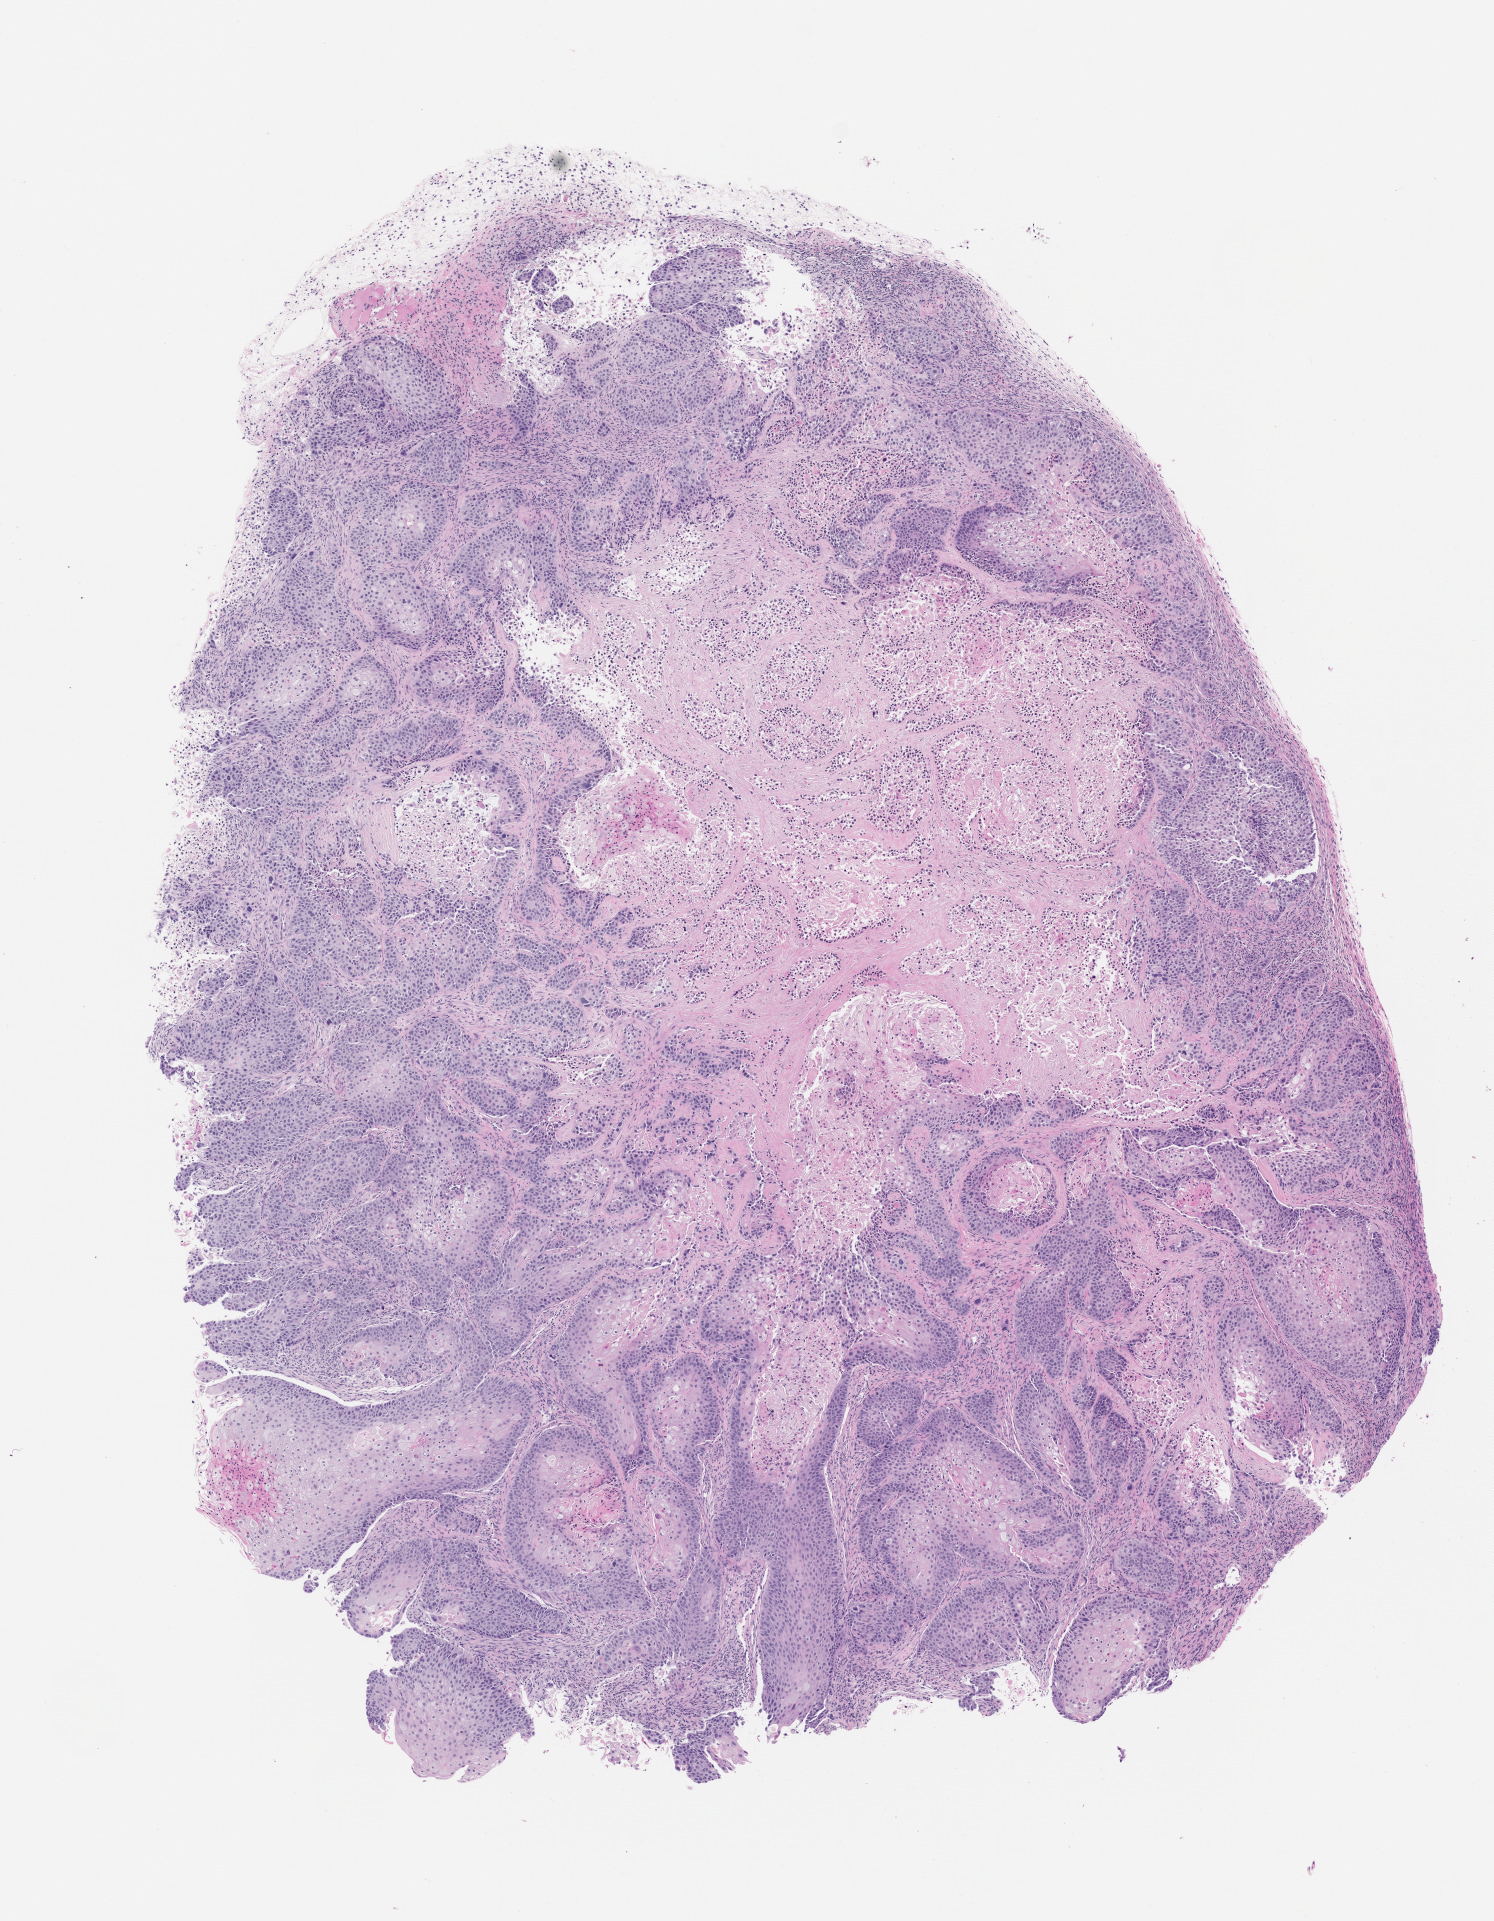
H&E whole-slide image of a patient-derived xenograft (PDX) tumor grown in a mouse, passage 2, a low-resolution overview of the entire scanned area, about 6.0 x 7.7 mm. FFPE section. Originating tumor site category: lung.
• originating patient diagnosis: Lung Squamous Cell Carcinoma